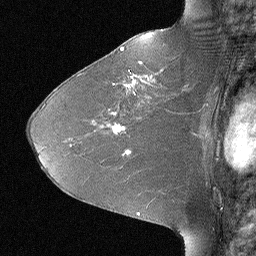
Breast MRI (dynamic contrast-enhanced), one sagittal slice; position 40 of 64 along the scan axis; dynamic contrast-enhanced study with each time point stored as its own series, time point 2 of 3 at this slice position (early post-contrast, ordered by acquisition time); 1.5 T; TE 4 ms, TR 30 ms; 2.25 mm slice thickness; 256 × 256 image matrix, field of view 180 × 180 mm. Patient: female, 46 years. From the clinical record (not read from this slice): setting: breast cancer imaged before/during neoadjuvant chemotherapy; receptor status: HR-positive, HER2-negative.
Annotated regions visible in this slice (semi-automatically segmented with operator editing):
- analysis volume of interest (the breast-tissue region the enhancement analysis was run in; not a lesion): box from (x=106, y=43) to (x=184, y=119) px
- tumour enhancement mask (voxels above the 90 % enhancement threshold inside the analysis volume of interest): (x=120, y=48)–(x=163, y=87)